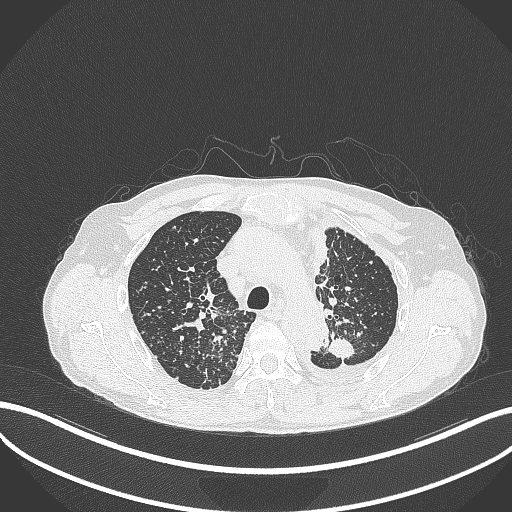
Chest CT, one axial slice. Position 262 of 325 along the scan axis. Lung window (W 1500 / L -600 HU). 1 mm slice thickness. 512 × 512 image matrix. Male patient, age 58 years. Case-level facts recorded for this patient, not image findings: clinical TNM (as recorded): T1c N3 M1.
Outlined on this slice (rectangle marked by the reading radiologist):
- lung tumour (recorded histology: adenocarcinoma): bounding box [x1, y1, x2, y2] px = [320, 331, 357, 362]